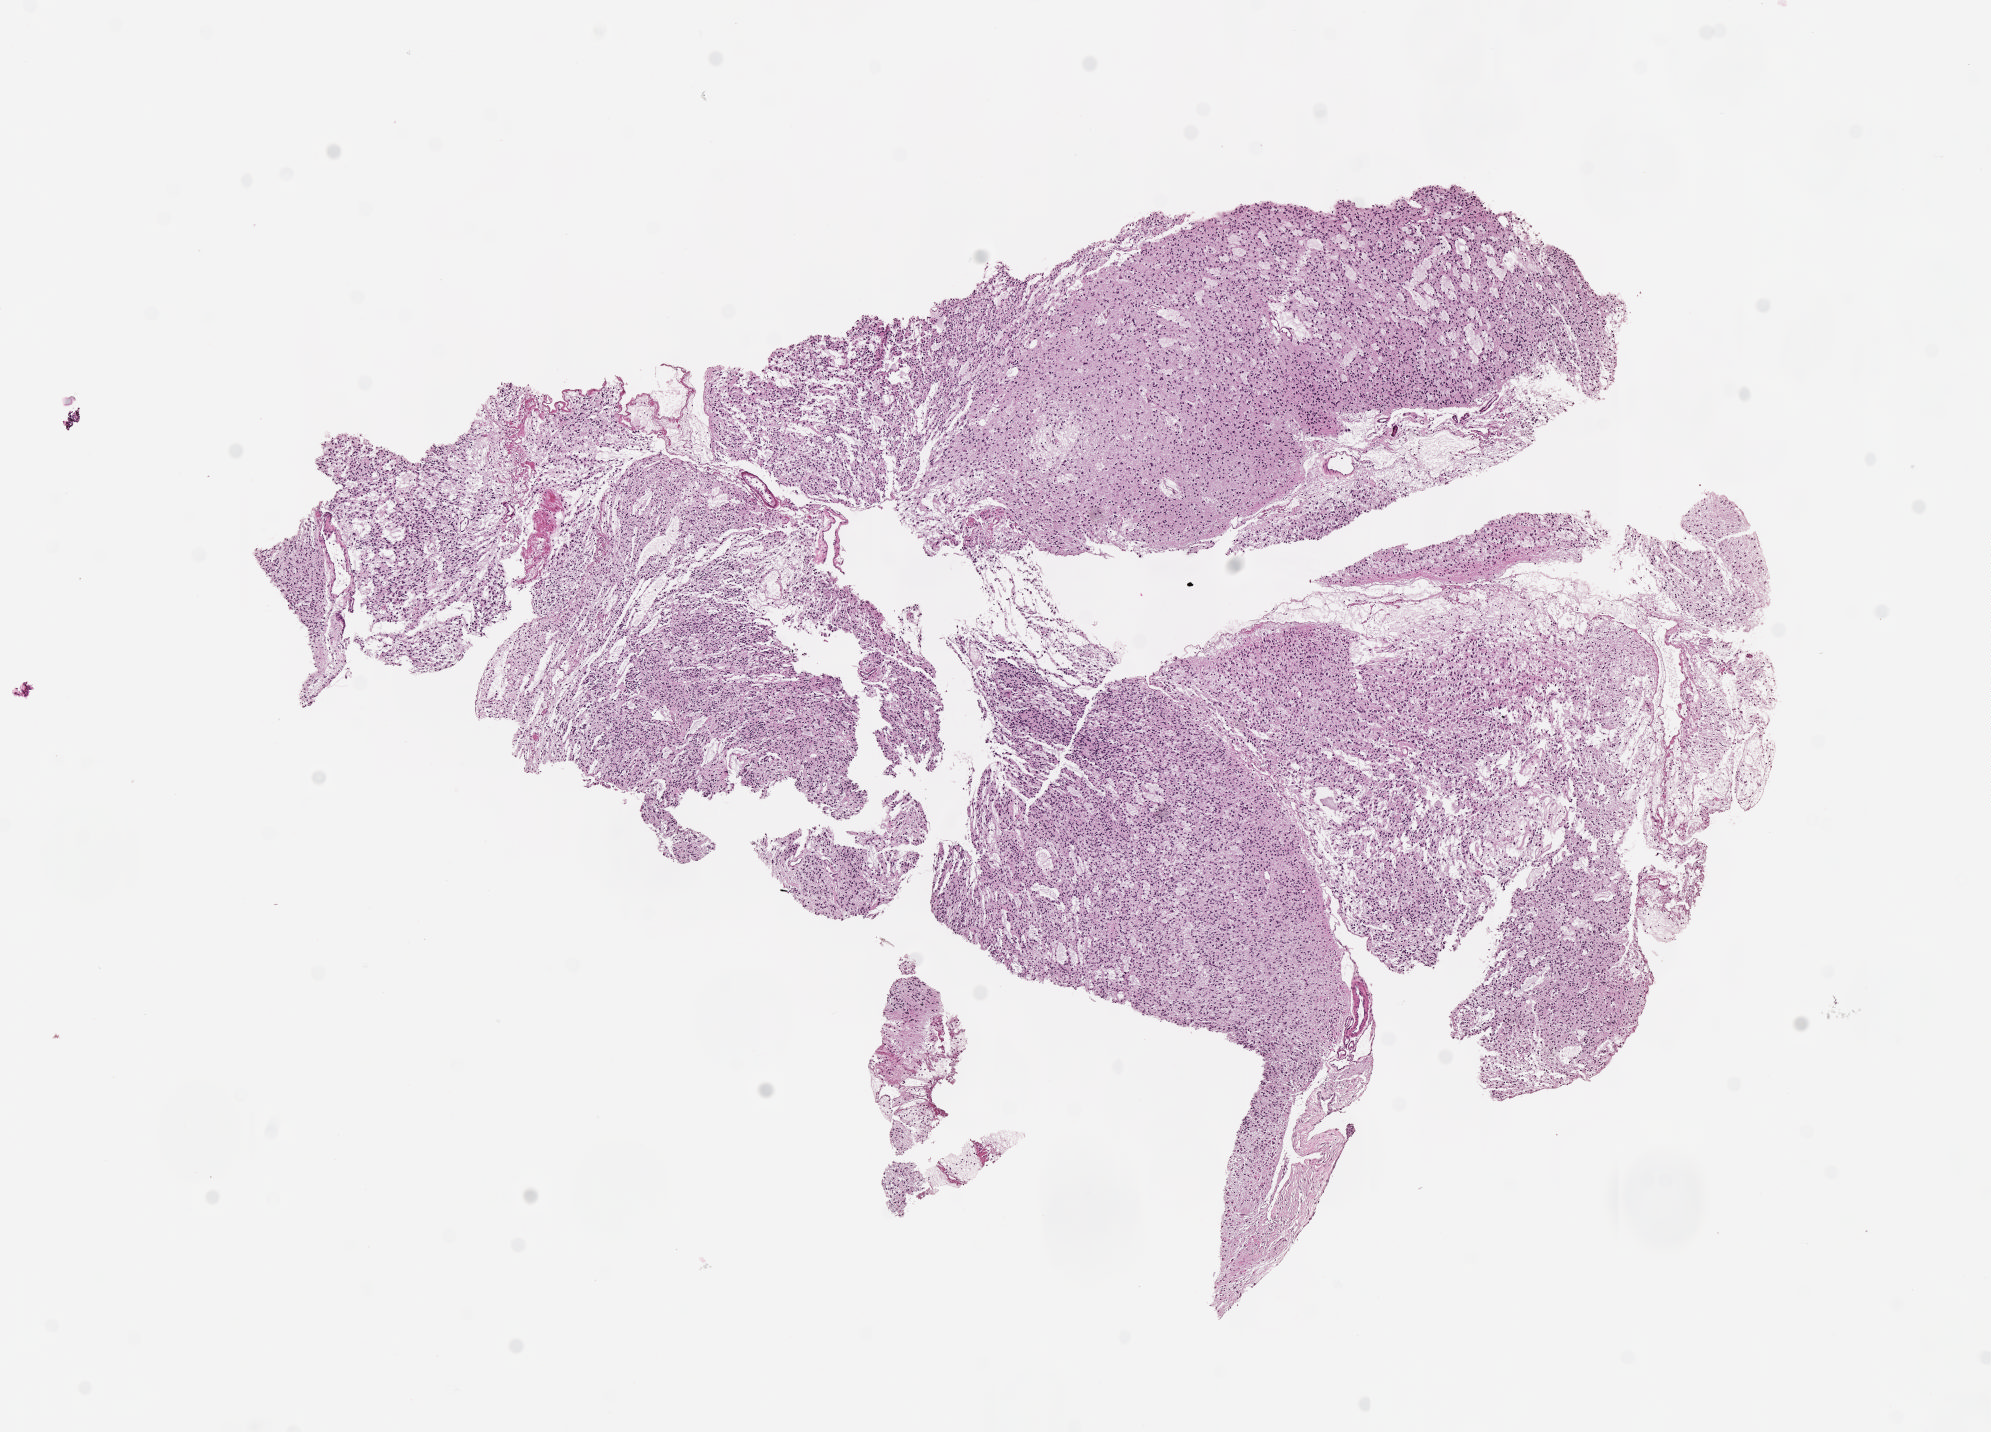
Whole-slide histology image, H&E, a low-resolution overview of the entire scanned area, about 8.1 x 5.8 mm (slide scanned at 40x), formalin-fixed paraffin-embedded (FFPE) diagnostic section, primary tumour sample from the brain. Male, age 35 years at initial diagnosis. Histologic grade: G3 (poorly differentiated).
* histologic diagnosis: Mixed glioma (cerebrum)
* laterality: right